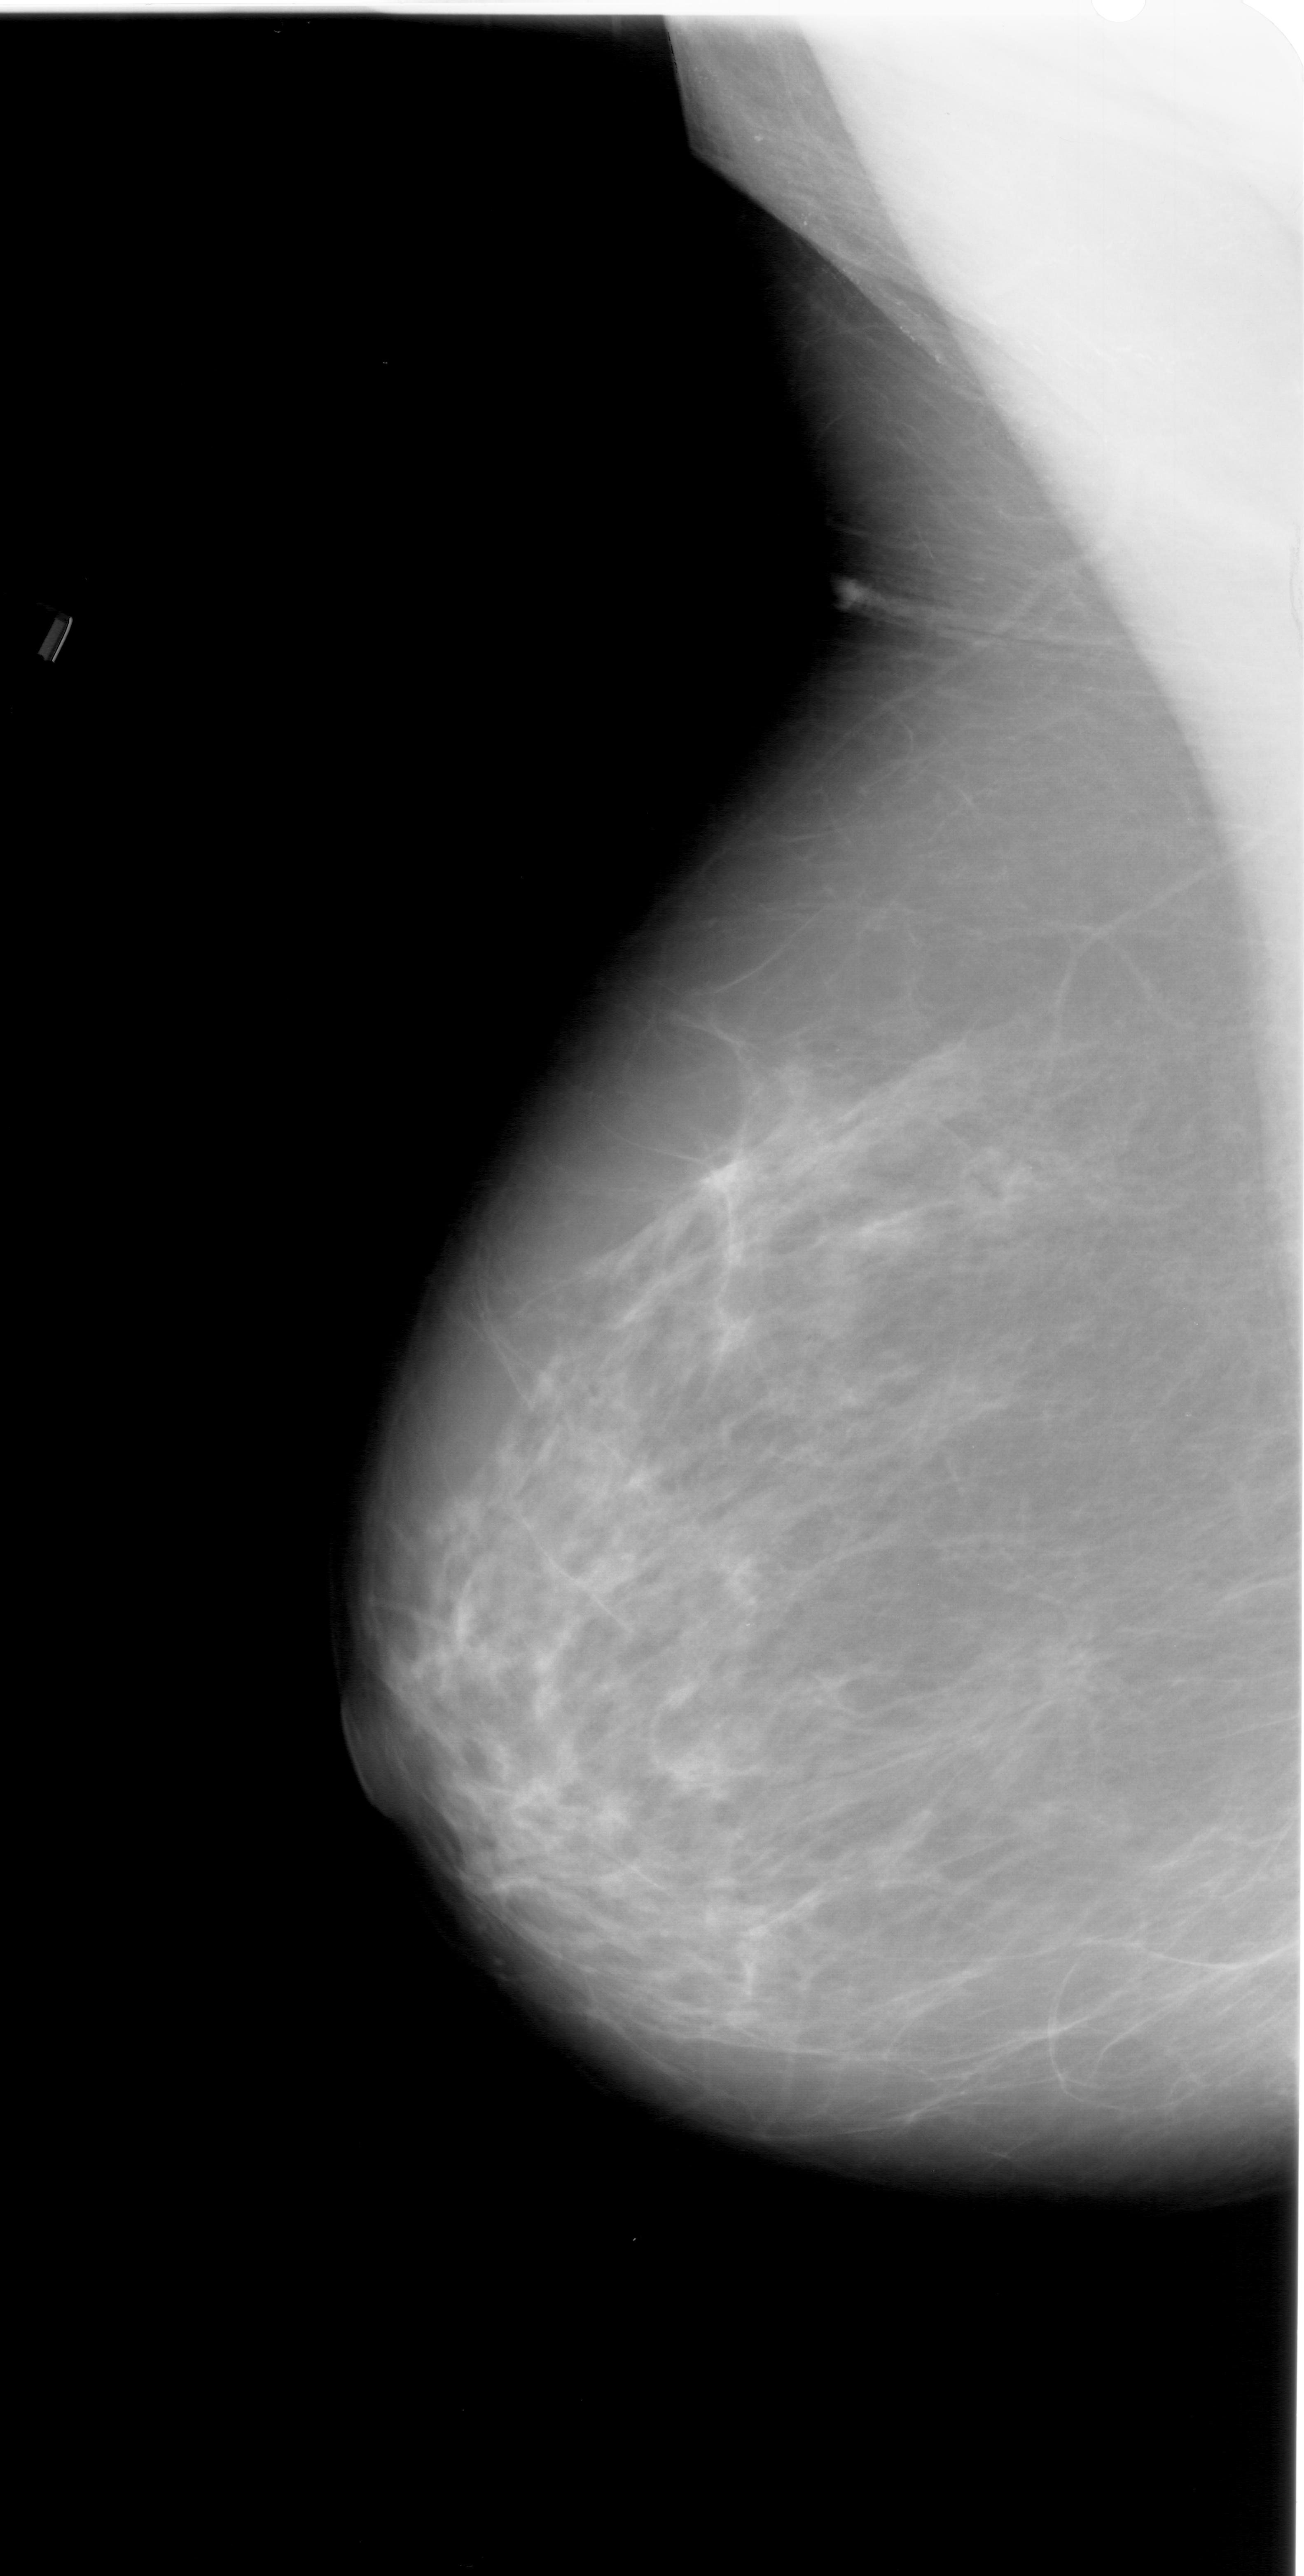
Scanned film-screen mammogram; left breast; MLO view; breast composition: heterogeneously dense (BI-RADS density category 3 of 4).
- Finding: mass, shape architectural distortion, margins ill defined; BI-RADS assessment category 4; pathology result (as recorded, not read from the image): benign.